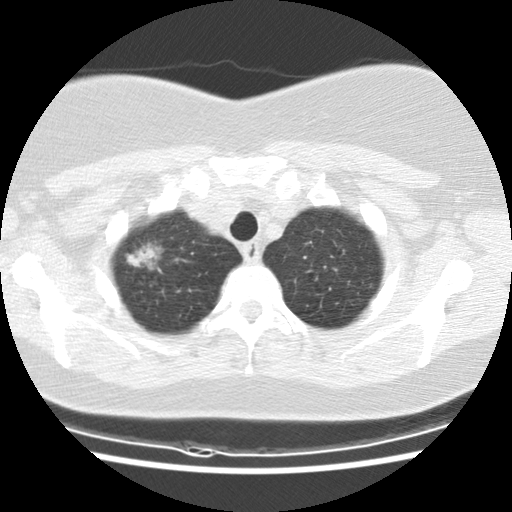
Axial slice from a low-dose chest CT screening exam, baseline screening round, lung window (W 1500 / L -600 HU), standard (soft-tissue) reconstruction kernel (STANDARD), slice 16 of 132 in the series, 512 × 512 image matrix, field of view 326 × 326 mm. Female, age 61 years at enrolment.
• Expert-annotated lung lesion, bounding box (x1, y1, x2, y2) in pixels: (115, 230, 177, 285).
• Reader record for this screening exam (exam-level; its link to the box is not recorded): non-calcified nodule or mass ≥4 mm, right upper lobe, 26 × 16 mm, spiculated (stellate) margins, mixed attenuation.
• Participant outcome: lung cancer diagnosed 47 days after this screen — bronchiolo-alveolar carcinoma, mixed mucinous and non-mucinous, right upper lobe, well differentiated (G1), stage IA (AJCC 6th edition), 25 mm at pathology.